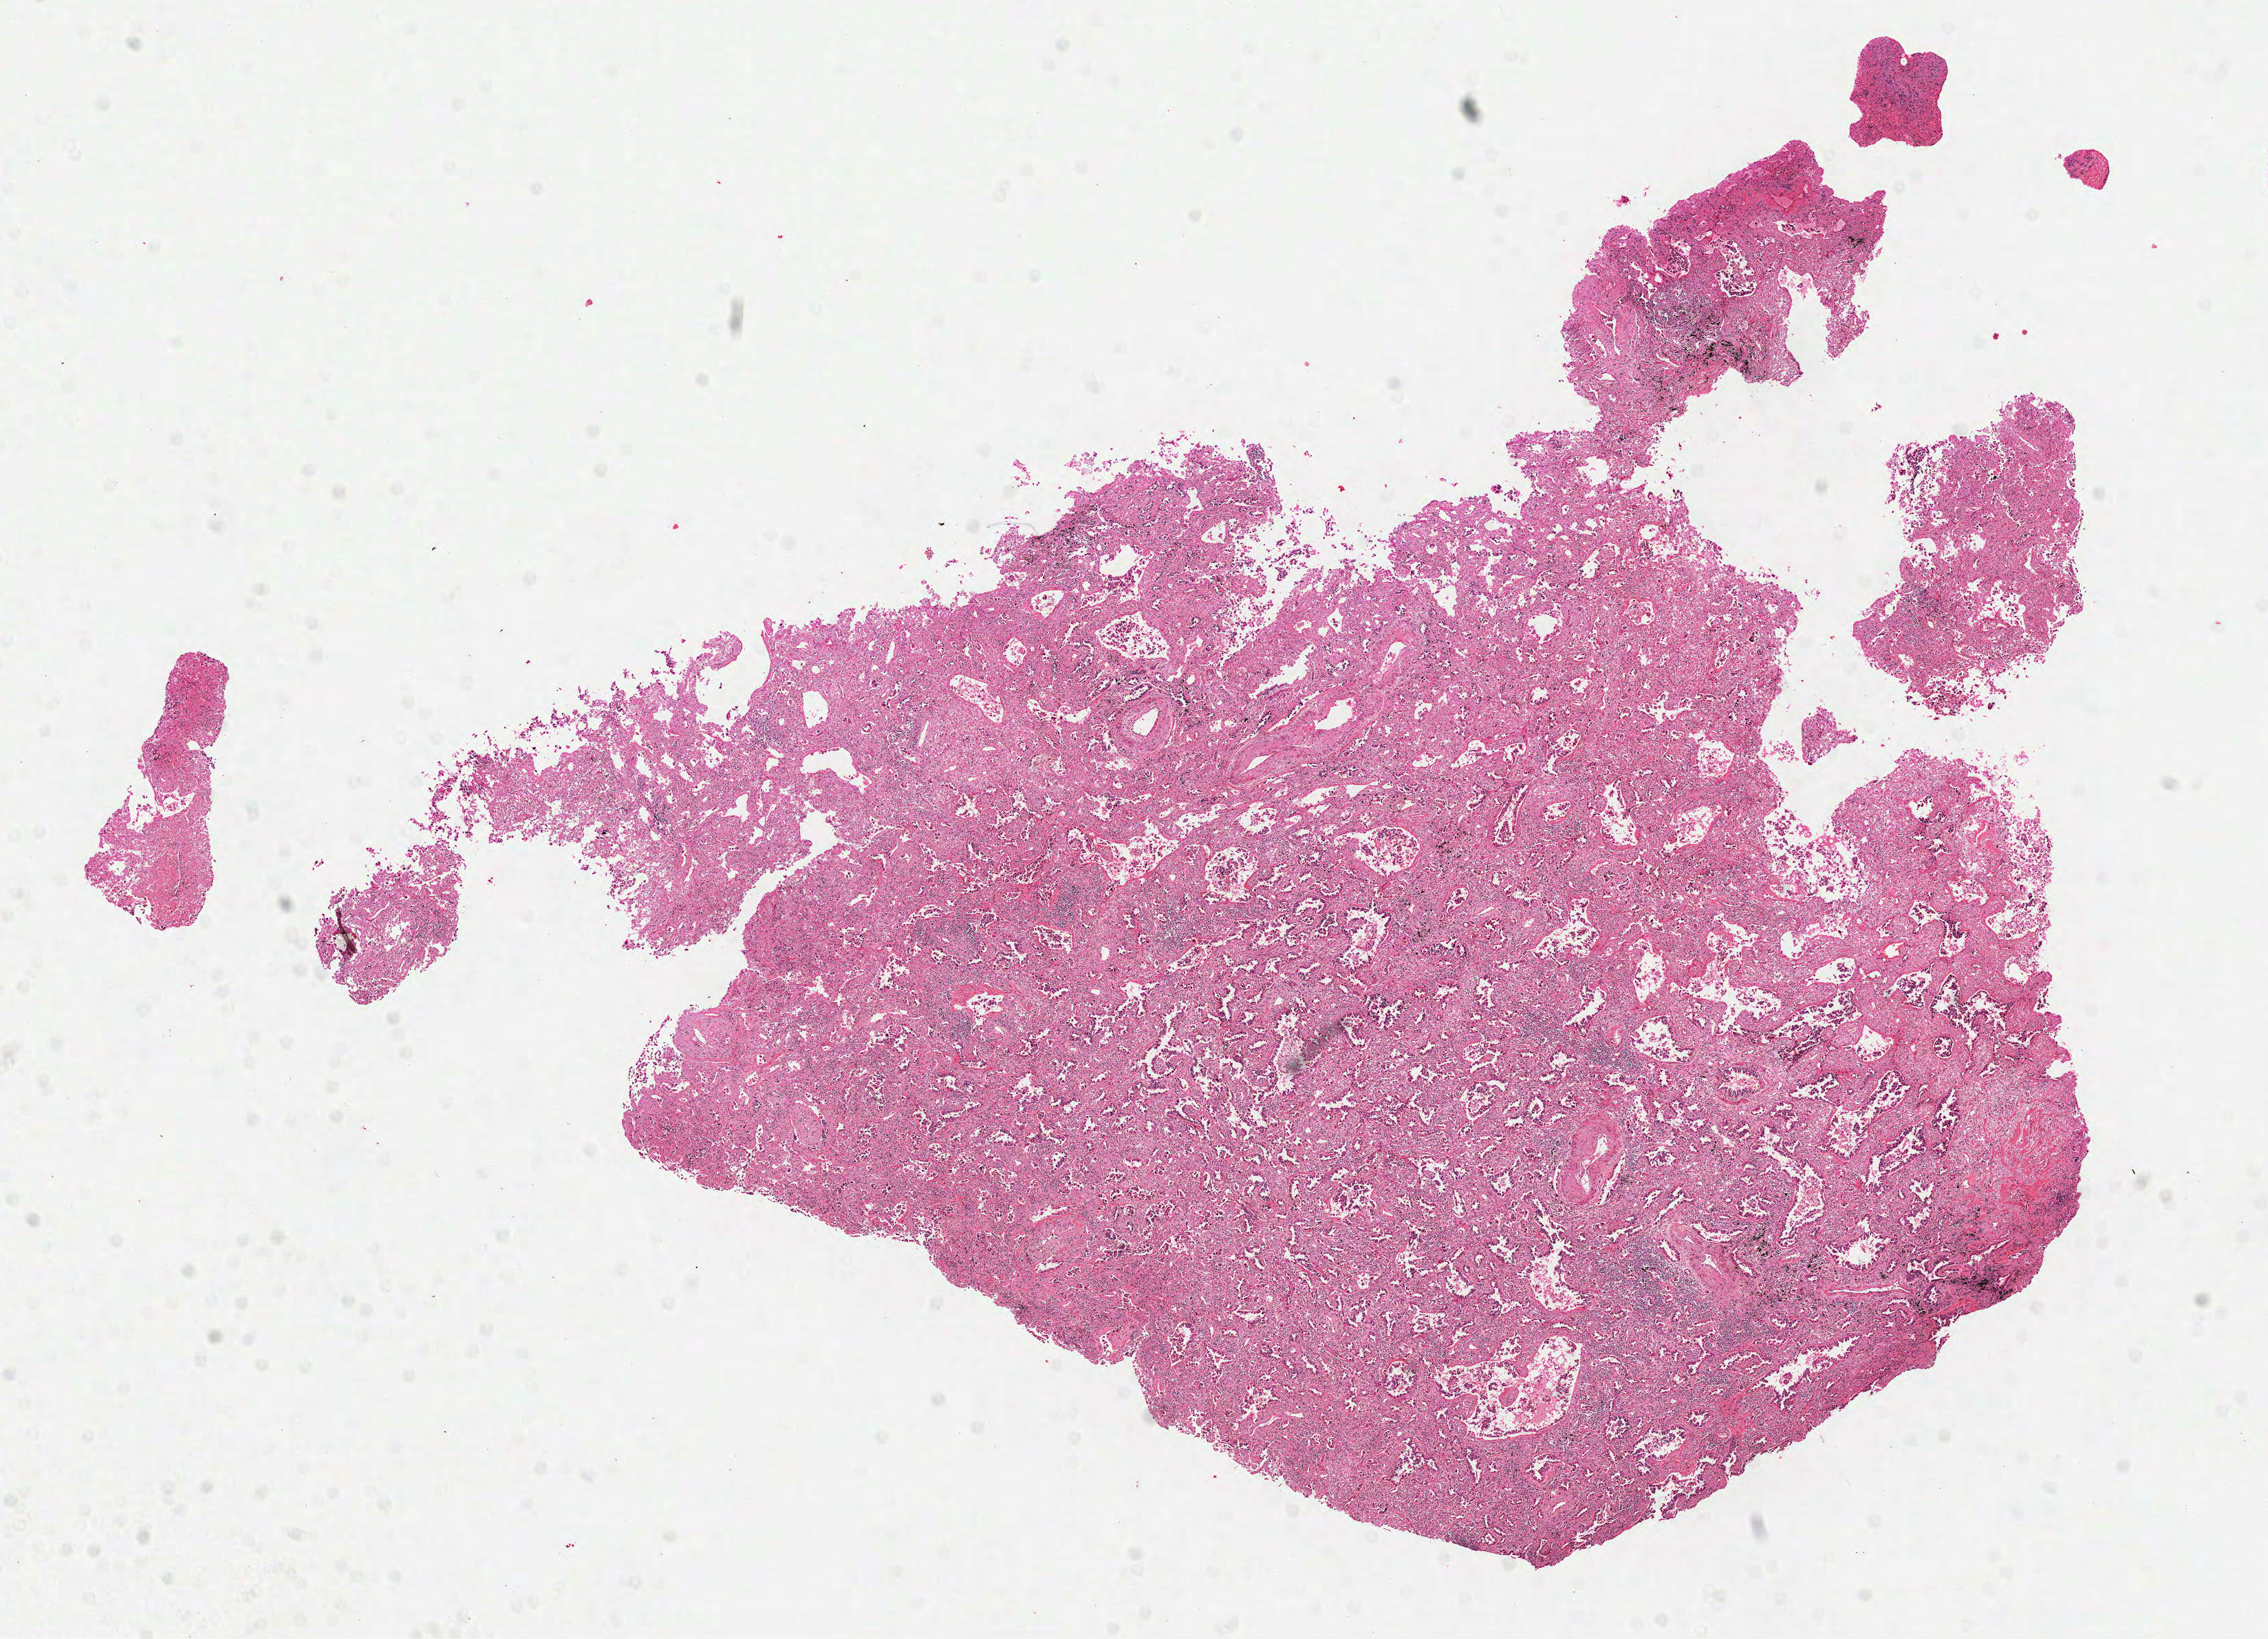
Digitized H&E-stained tissue section (whole slide), a low-resolution overview of the entire scanned area, about 13.3 x 9.6 mm; formalin-fixed paraffin-embedded (FFPE) diagnostic section; lung, primary tumour sample. Female, age 61 years at initial diagnosis.
Diagnosis: Adenocarcinoma, NOS.